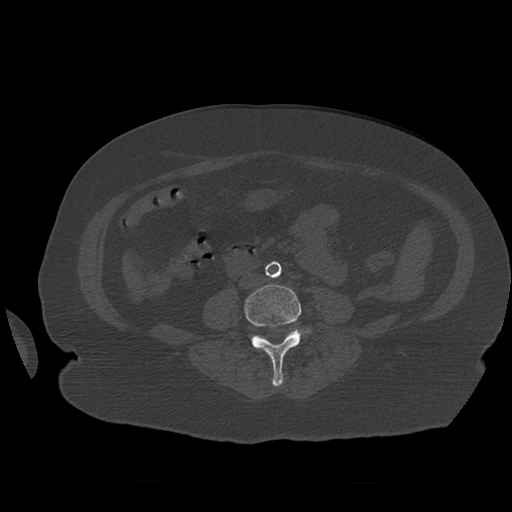
CT including the spine, one axial slice; slice 203 of 399 in the series (ordered by position); reconstruction kernel STANDARD; 120 kVp; bone window (W 1800 / L 400 HU); 1.25 mm slice thickness; 512 × 512 image matrix. Patient age 81 years. Case-level facts recorded for this patient, not image findings: primary cancer: renal; vertebrae with lytic lesions (as recorded): L1.
Outlined on this slice (semi-automatic segmentation, software-assisted and operator-edited):
- L4 vertebra: bounding box (x1, y1, x2, y2) in pixels: (245, 284, 312, 387)
- L5 vertebra: (290, 329, 295, 334)